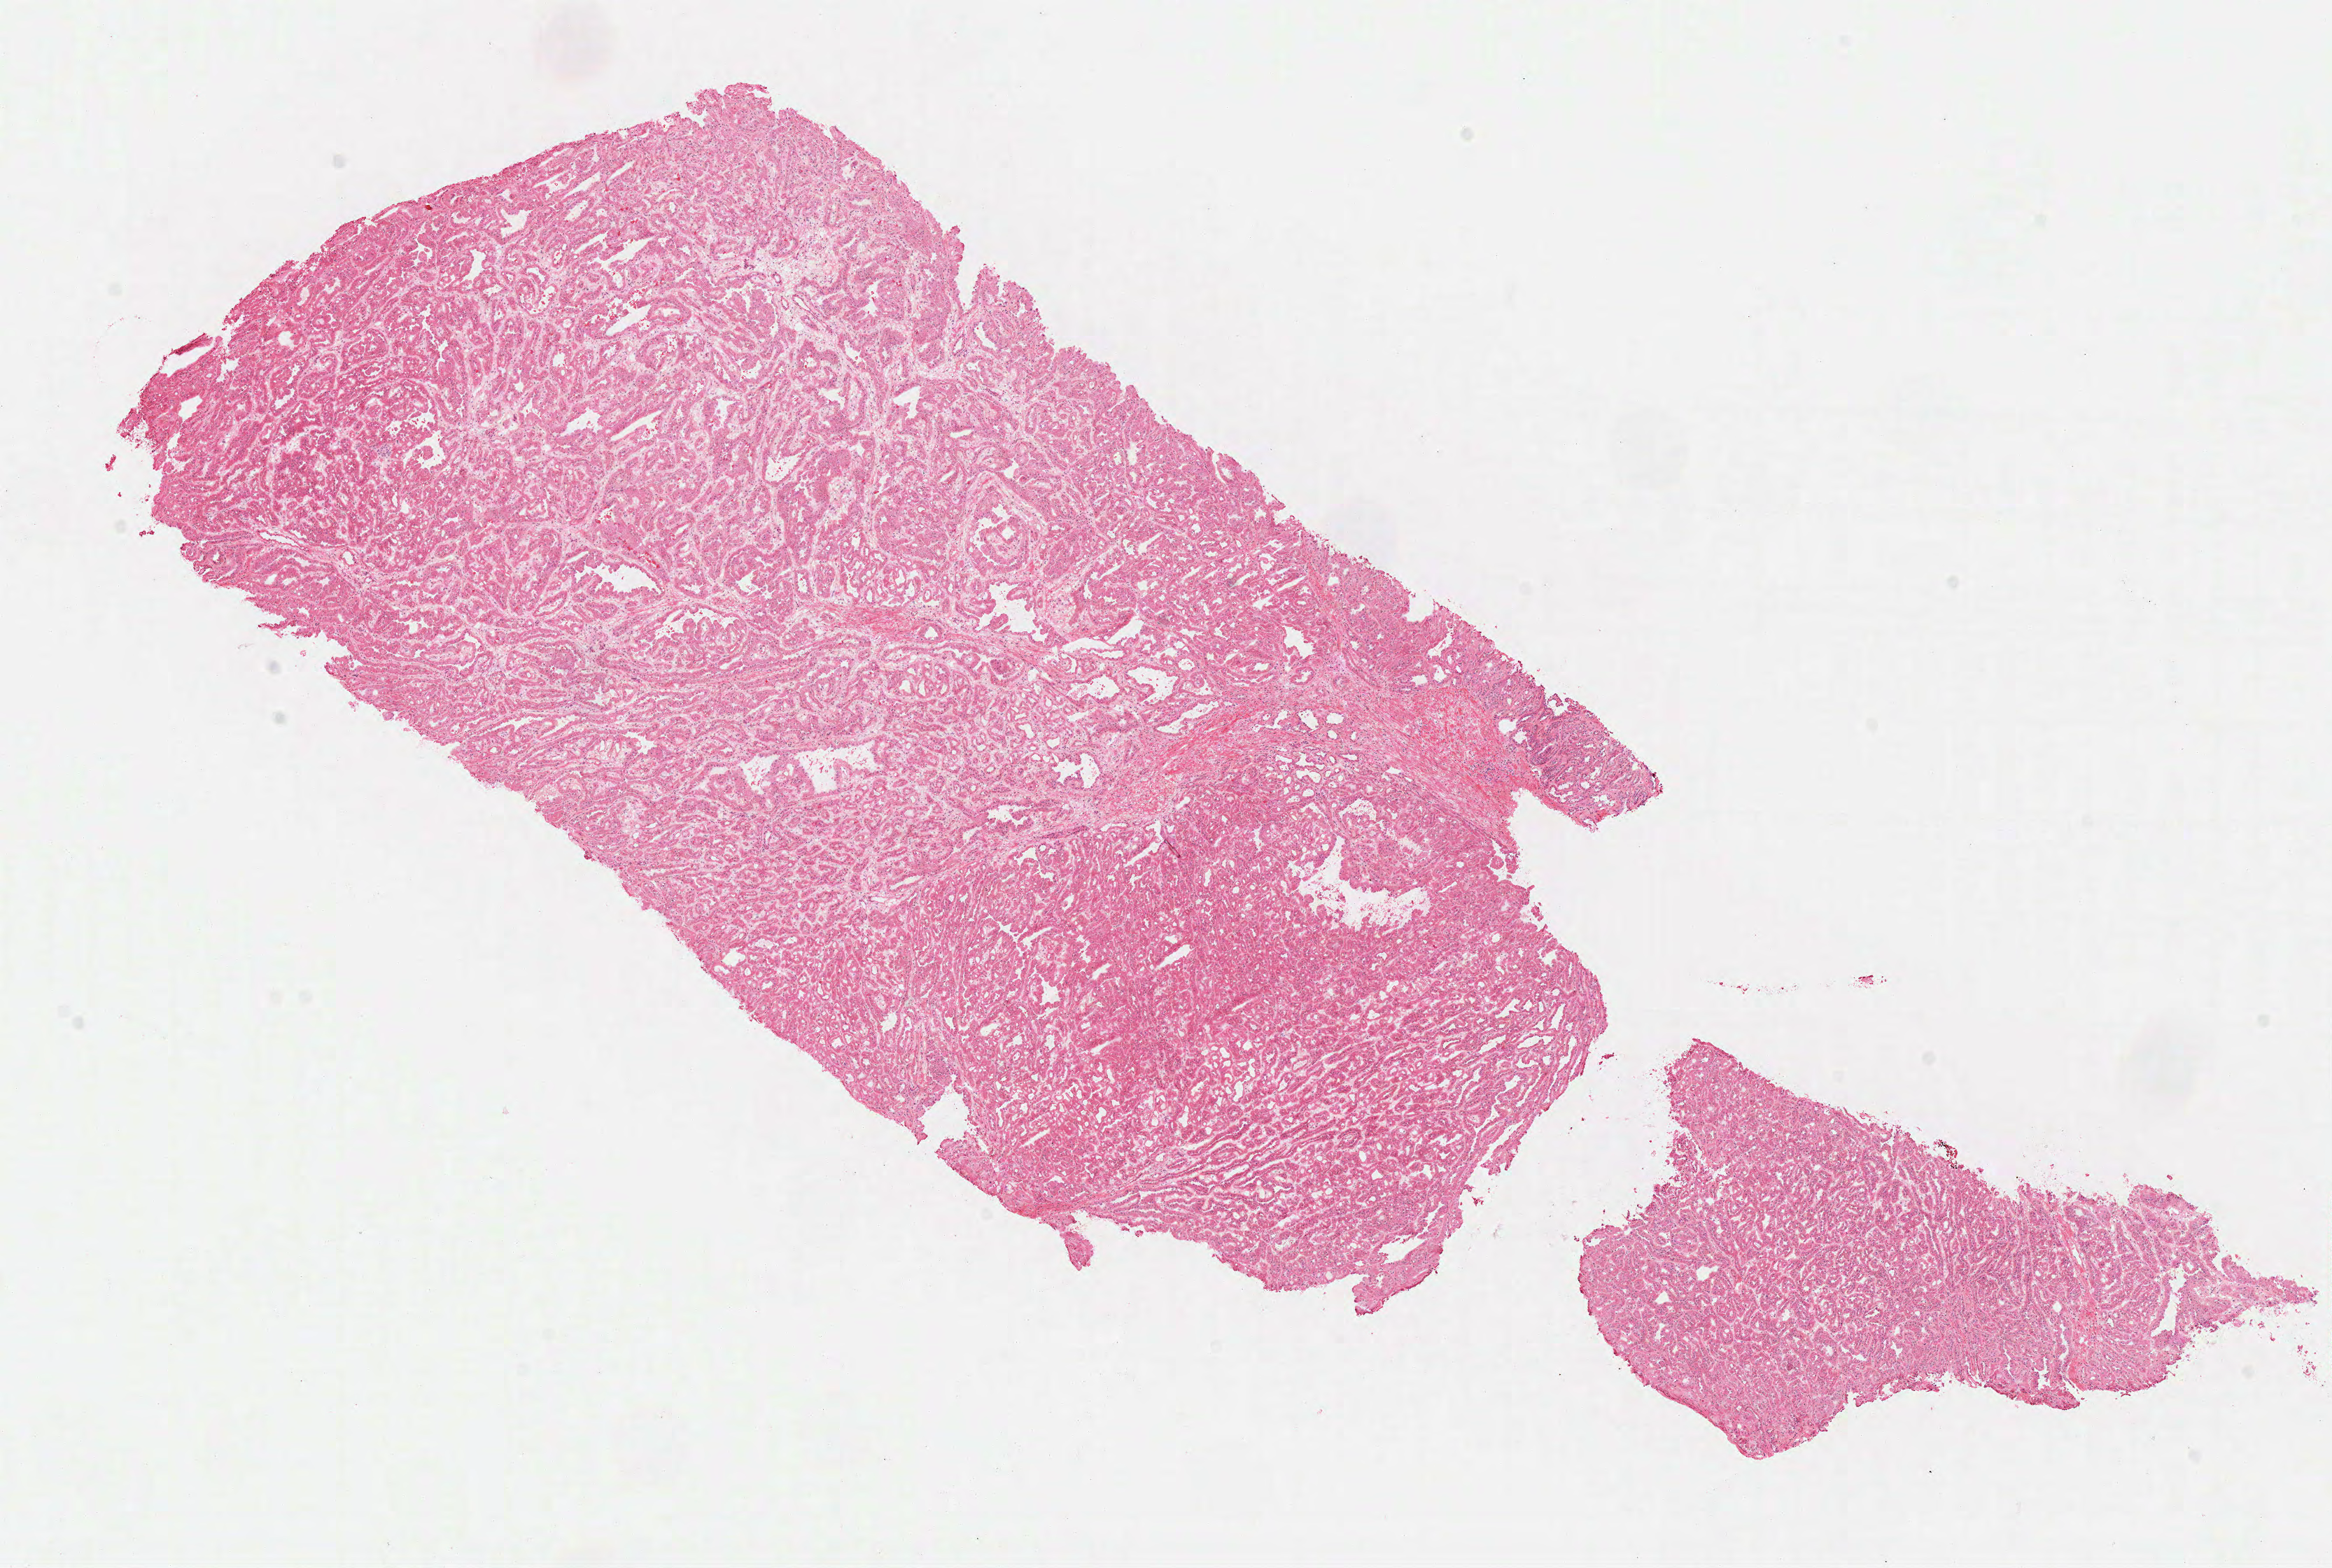
Digitized H&E-stained tissue section (whole slide) — low-resolution overview of the scanned area, about 13.1 x 8.8 mm (slide scanned at 40x), frozen section from the top of the tissue portion, sample: primary tumour, kidney. Patient: female, age at initial diagnosis 79 years. Pathologist review of this section (percent, as recorded): tumour cells 95%, tumour nuclei 85%, normal cells 0%, stromal cells 5%, necrosis 0%.
* AJCC pathologic stage: I (6th edition)
* laterality: right
* histologic diagnosis: Papillary adenocarcinoma, NOS